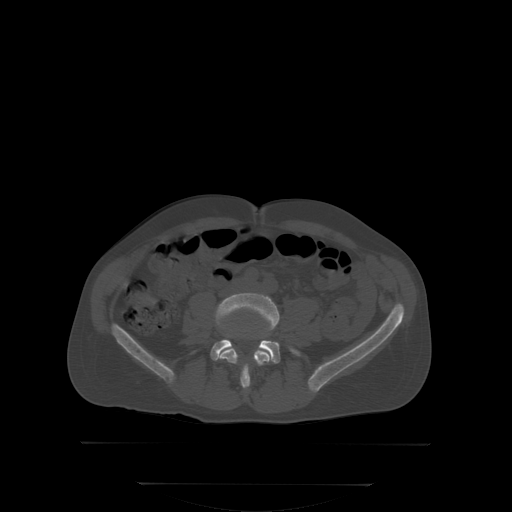
CT including the spine, one axial slice. Position 102 of 350 along the scan axis. Bone window (W 1800 / L 400 HU). 2.5 mm slice thickness. 512 × 512 image matrix, field of view 500 × 500 mm. Patient: male, 58 years. Case-level facts recorded for this patient, not image findings: primary cancer: prostate; vertebrae with lytic lesions (as recorded): L1.
Structures marked on this image (semi-automatically segmented with operator editing):
- L4 vertebra: box from (x=216, y=293) to (x=278, y=389) px
- L5 vertebra: (x=211, y=339)–(x=296, y=362)